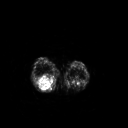
FDG PET of an extremity soft-tissue mass (from a PET/CT study), one axial slice; position 170 of 267 along the scan axis; 3.27 mm slice thickness; 128 × 128 image matrix, field of view 500 × 500 mm. Patient: female, 62 years. Case-level facts recorded for this patient, not image findings: histological type: liposarcoma; site of the primary tumour: right thigh.
Outlined on this slice (expert contour drawn on MRI and transferred to this co-registered scan by the dataset authors):
- gross tumour volume (mass): bounding box (x1, y1, x2, y2) in pixels: (37, 75, 55, 91)